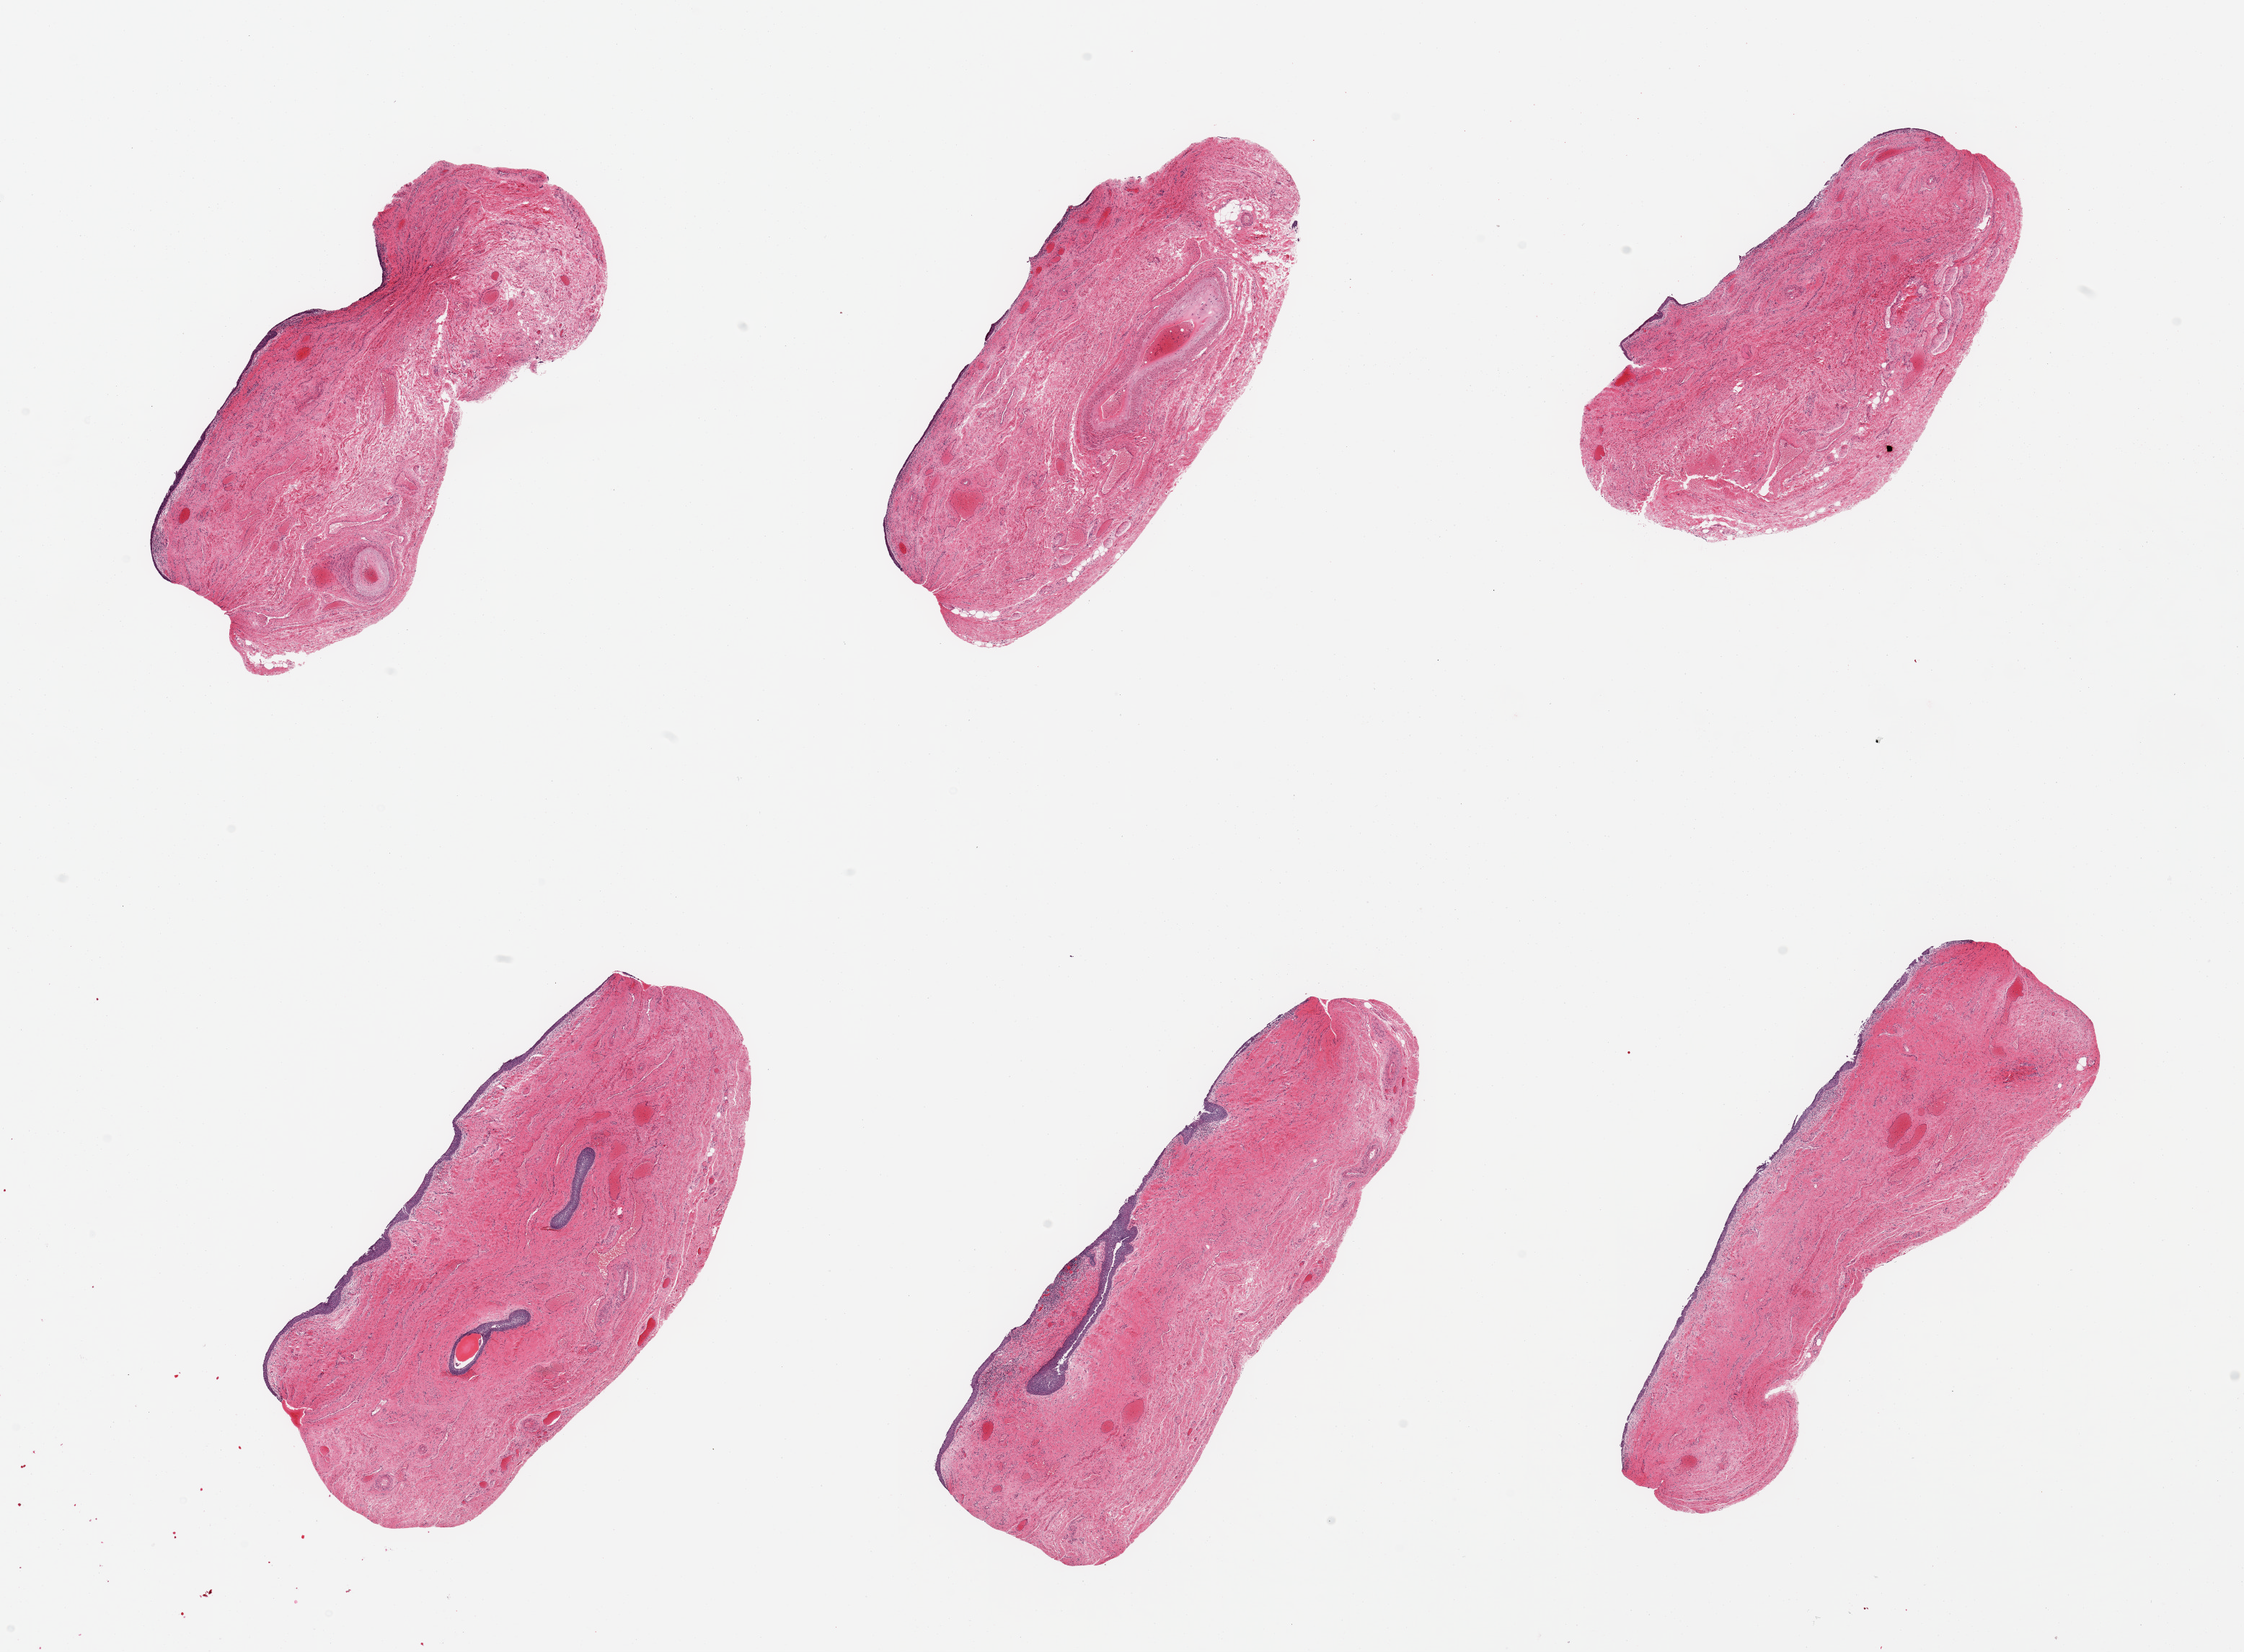
H&E whole-slide image, a low-resolution overview of the entire scanned area, about 24.6 x 18.1 mm, PAXgene-fixed paraffin-embedded (PFPE) section, target tissue: vagina, tissue donor sample. Donor: female.
Review note (as recorded): 6 pieces; partly sloughed atrophic epithelium.